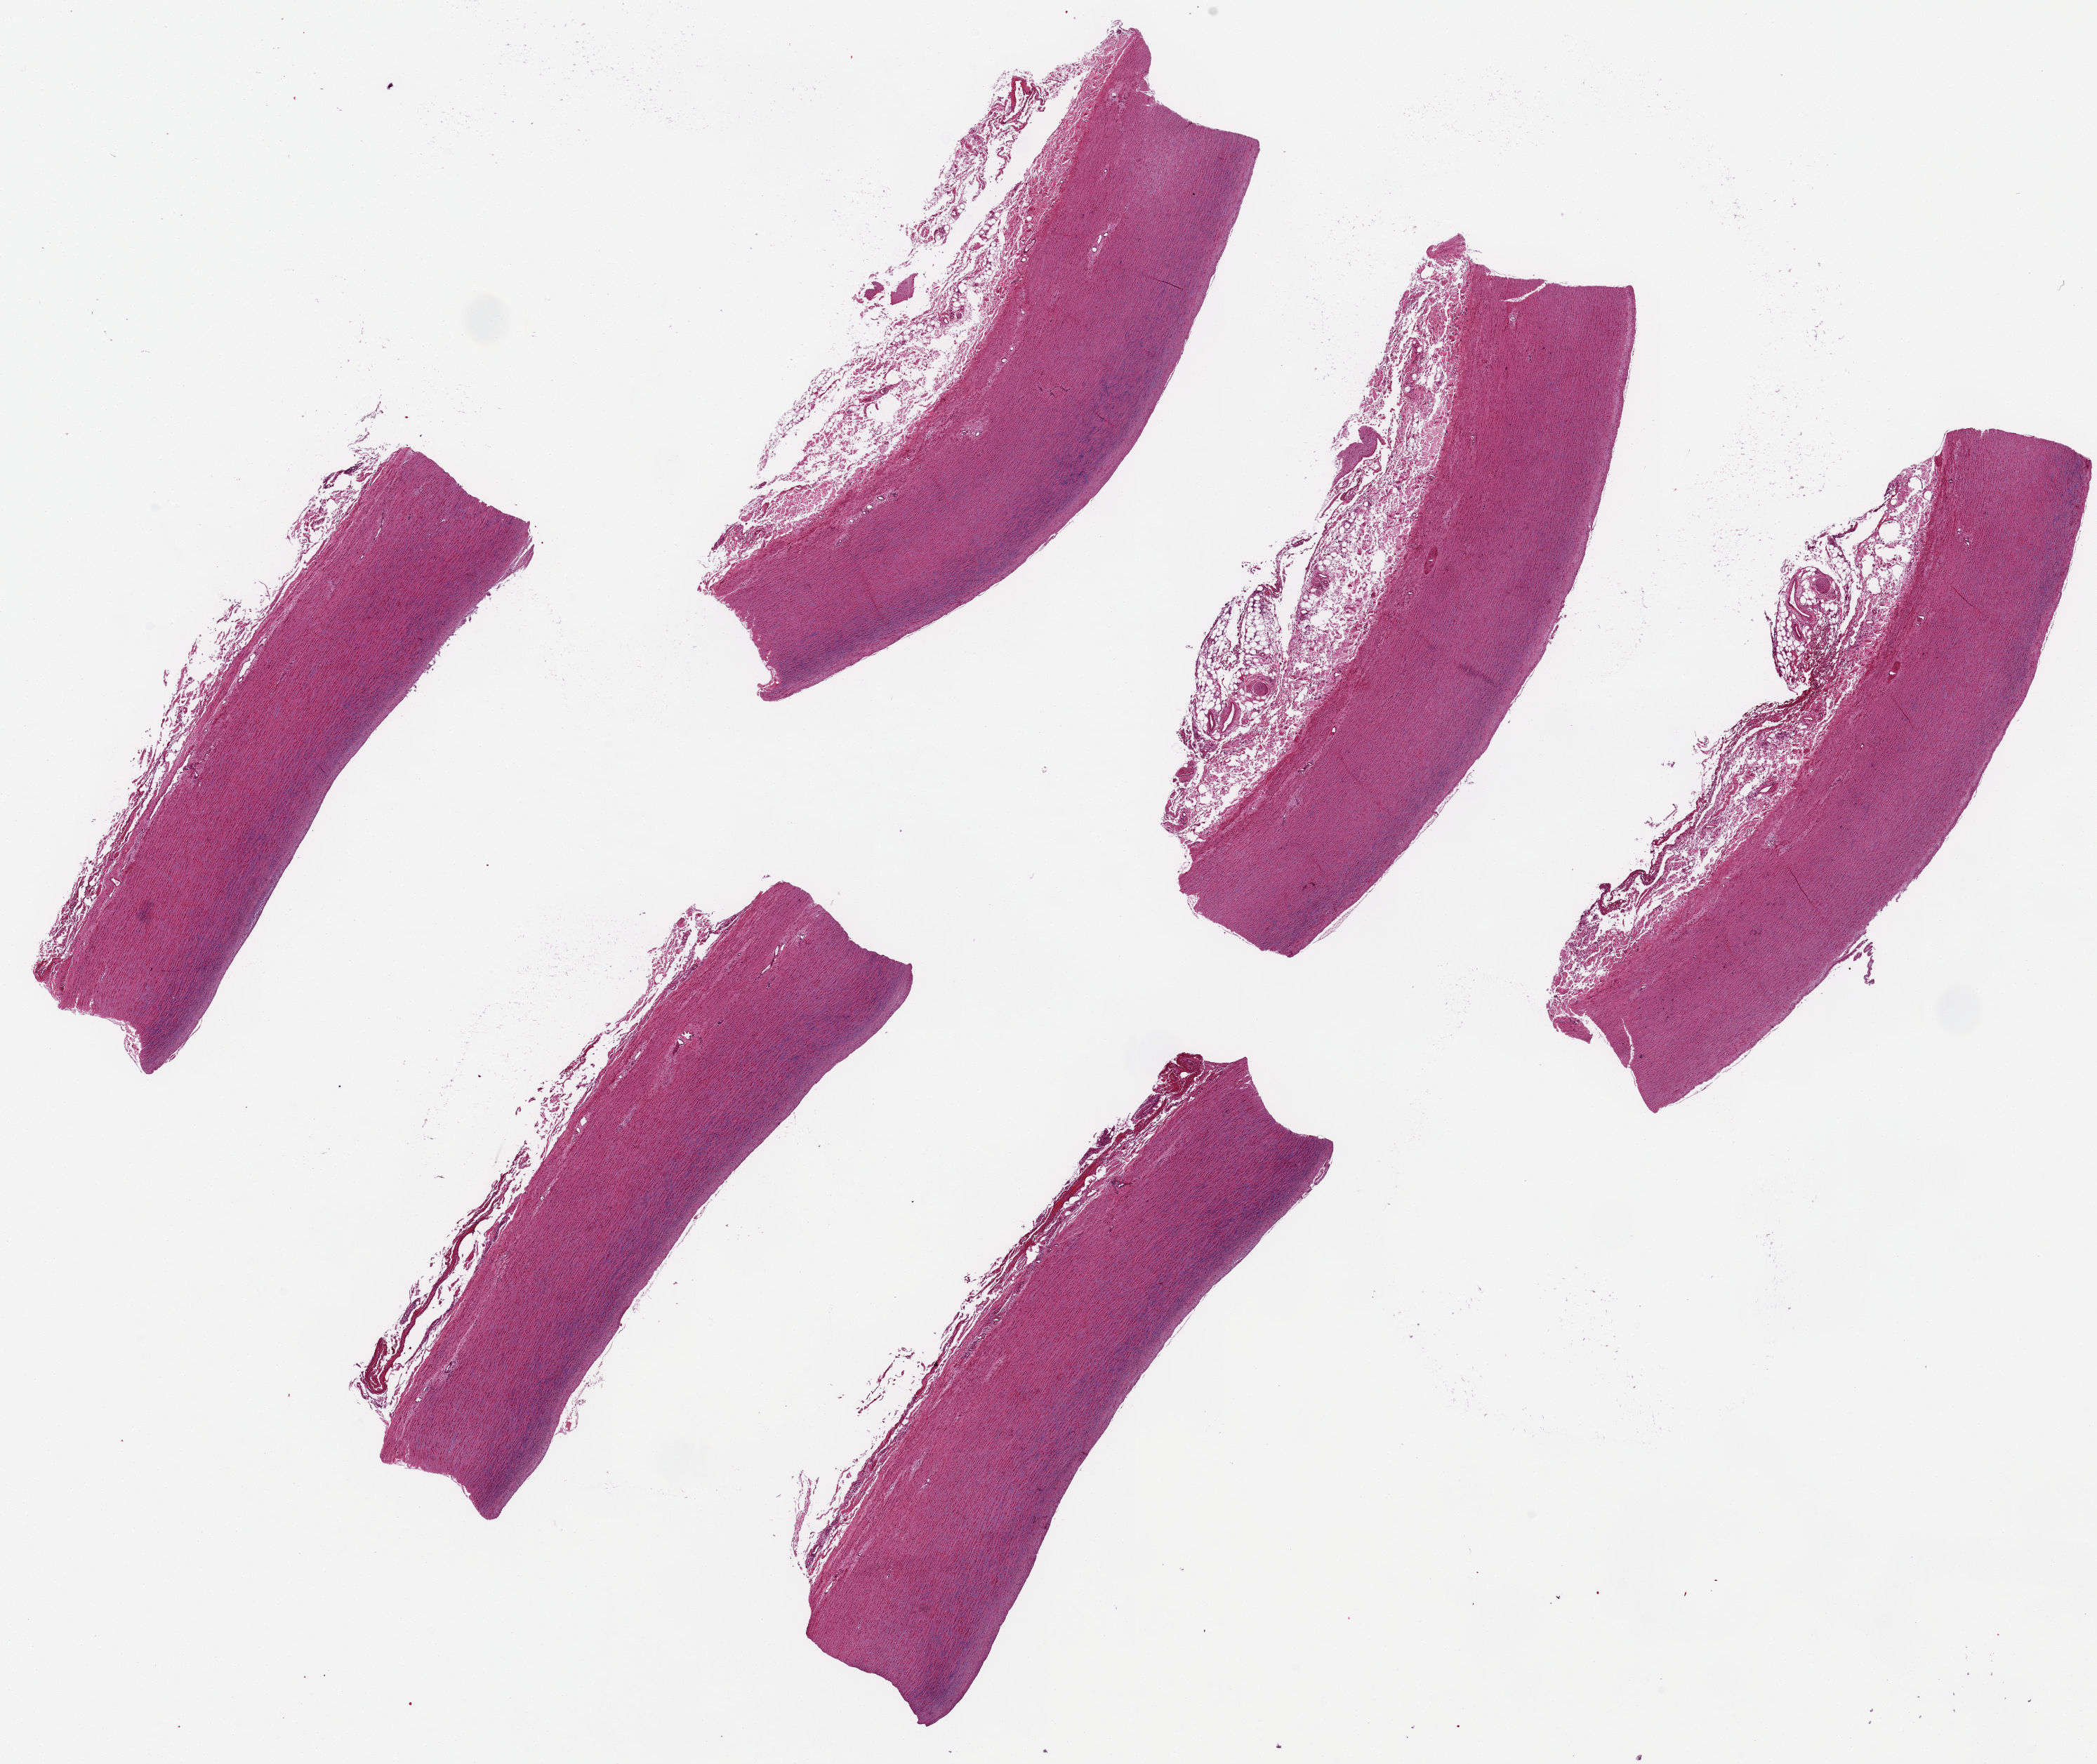
H&E whole-slide image, whole scanned area (about 23.6 x 19.9 mm, slide scanned at 20x) shown as a low-resolution overview; PAXgene-fixed paraffin-embedded (PFPE) section; sampled site (target tissue): aorta; donor tissue sample. Donor: female.
Review note (as recorded): 6 pieces, ~8x2mm. Several have up to ~1mm adherent fibroadipose tissue.